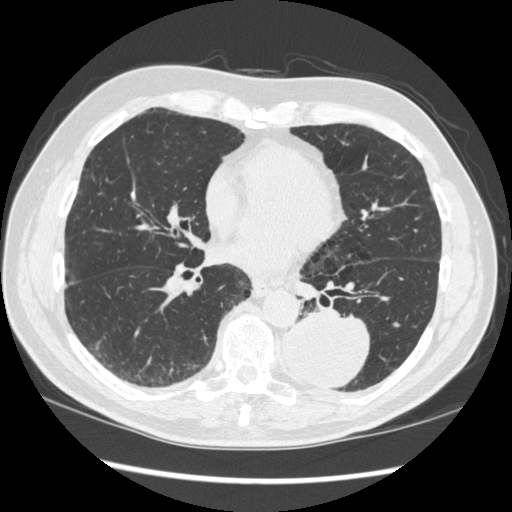
Low-dose screening chest CT, axial slice. First (baseline) screen. Lung window (W 1500 / L -600 HU). 1.25 mm slice thickness. Slice 144 of 348 in the series. 512 × 512 image matrix, field of view 360 × 360 mm. Male, age 72 years at enrolment.
Lesion marked by an expert reader, bounding box (x1, y1, x2, y2) in pixels: (269, 301, 373, 392). The screening reader recorded 2 non-calcified nodules or masses ≥4 mm on this exam (left lower lobe, right middle lobe); which of them this box marks is not recorded. Participant outcome: lung cancer diagnosed 37 days after this screen — squamous cell carcinoma, NOS, left lower lobe, stage IIIA (AJCC 6th edition), 60 mm at pathology.